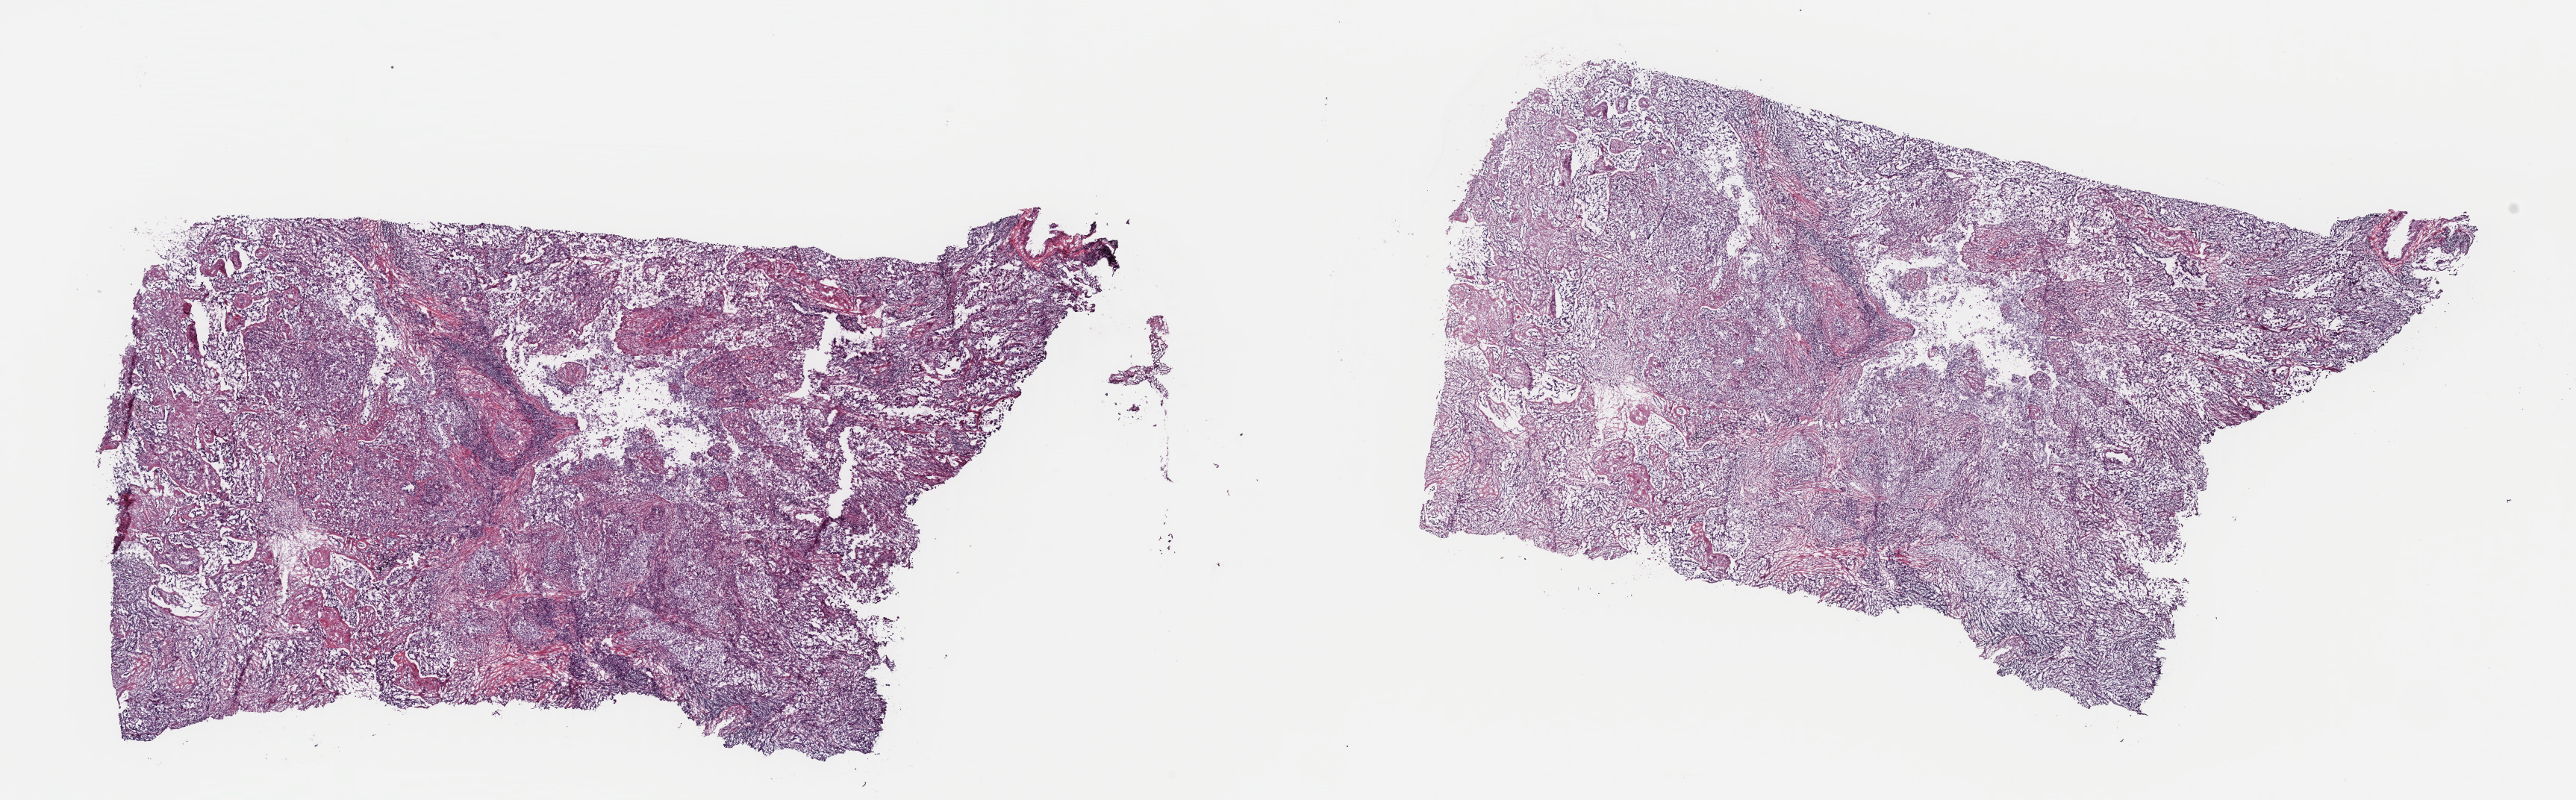
Digitized Hematoxylin and eosin (H&E) stained tissue section (whole slide) — low-resolution overview of the scanned area, about 27.2 x 8.5 mm (from a 40x scan). Frozen section from the top of the tissue portion. Lung, primary tumour sample. Patient: female, age at initial diagnosis 56 years. Composition of this section per pathologist review: tumour cells 100%, tumour nuclei 70%, normal cells 0%, stromal cells 0%, necrosis 0%. Inflammatory infiltration, as recorded: lymphocyte infiltration 0%, monocyte infiltration 0%, neutrophil infiltration 0%.
AJCC pathologic stage: IIB. Pathologic diagnosis: Adenocarcinoma, NOS (lower lobe, lung).